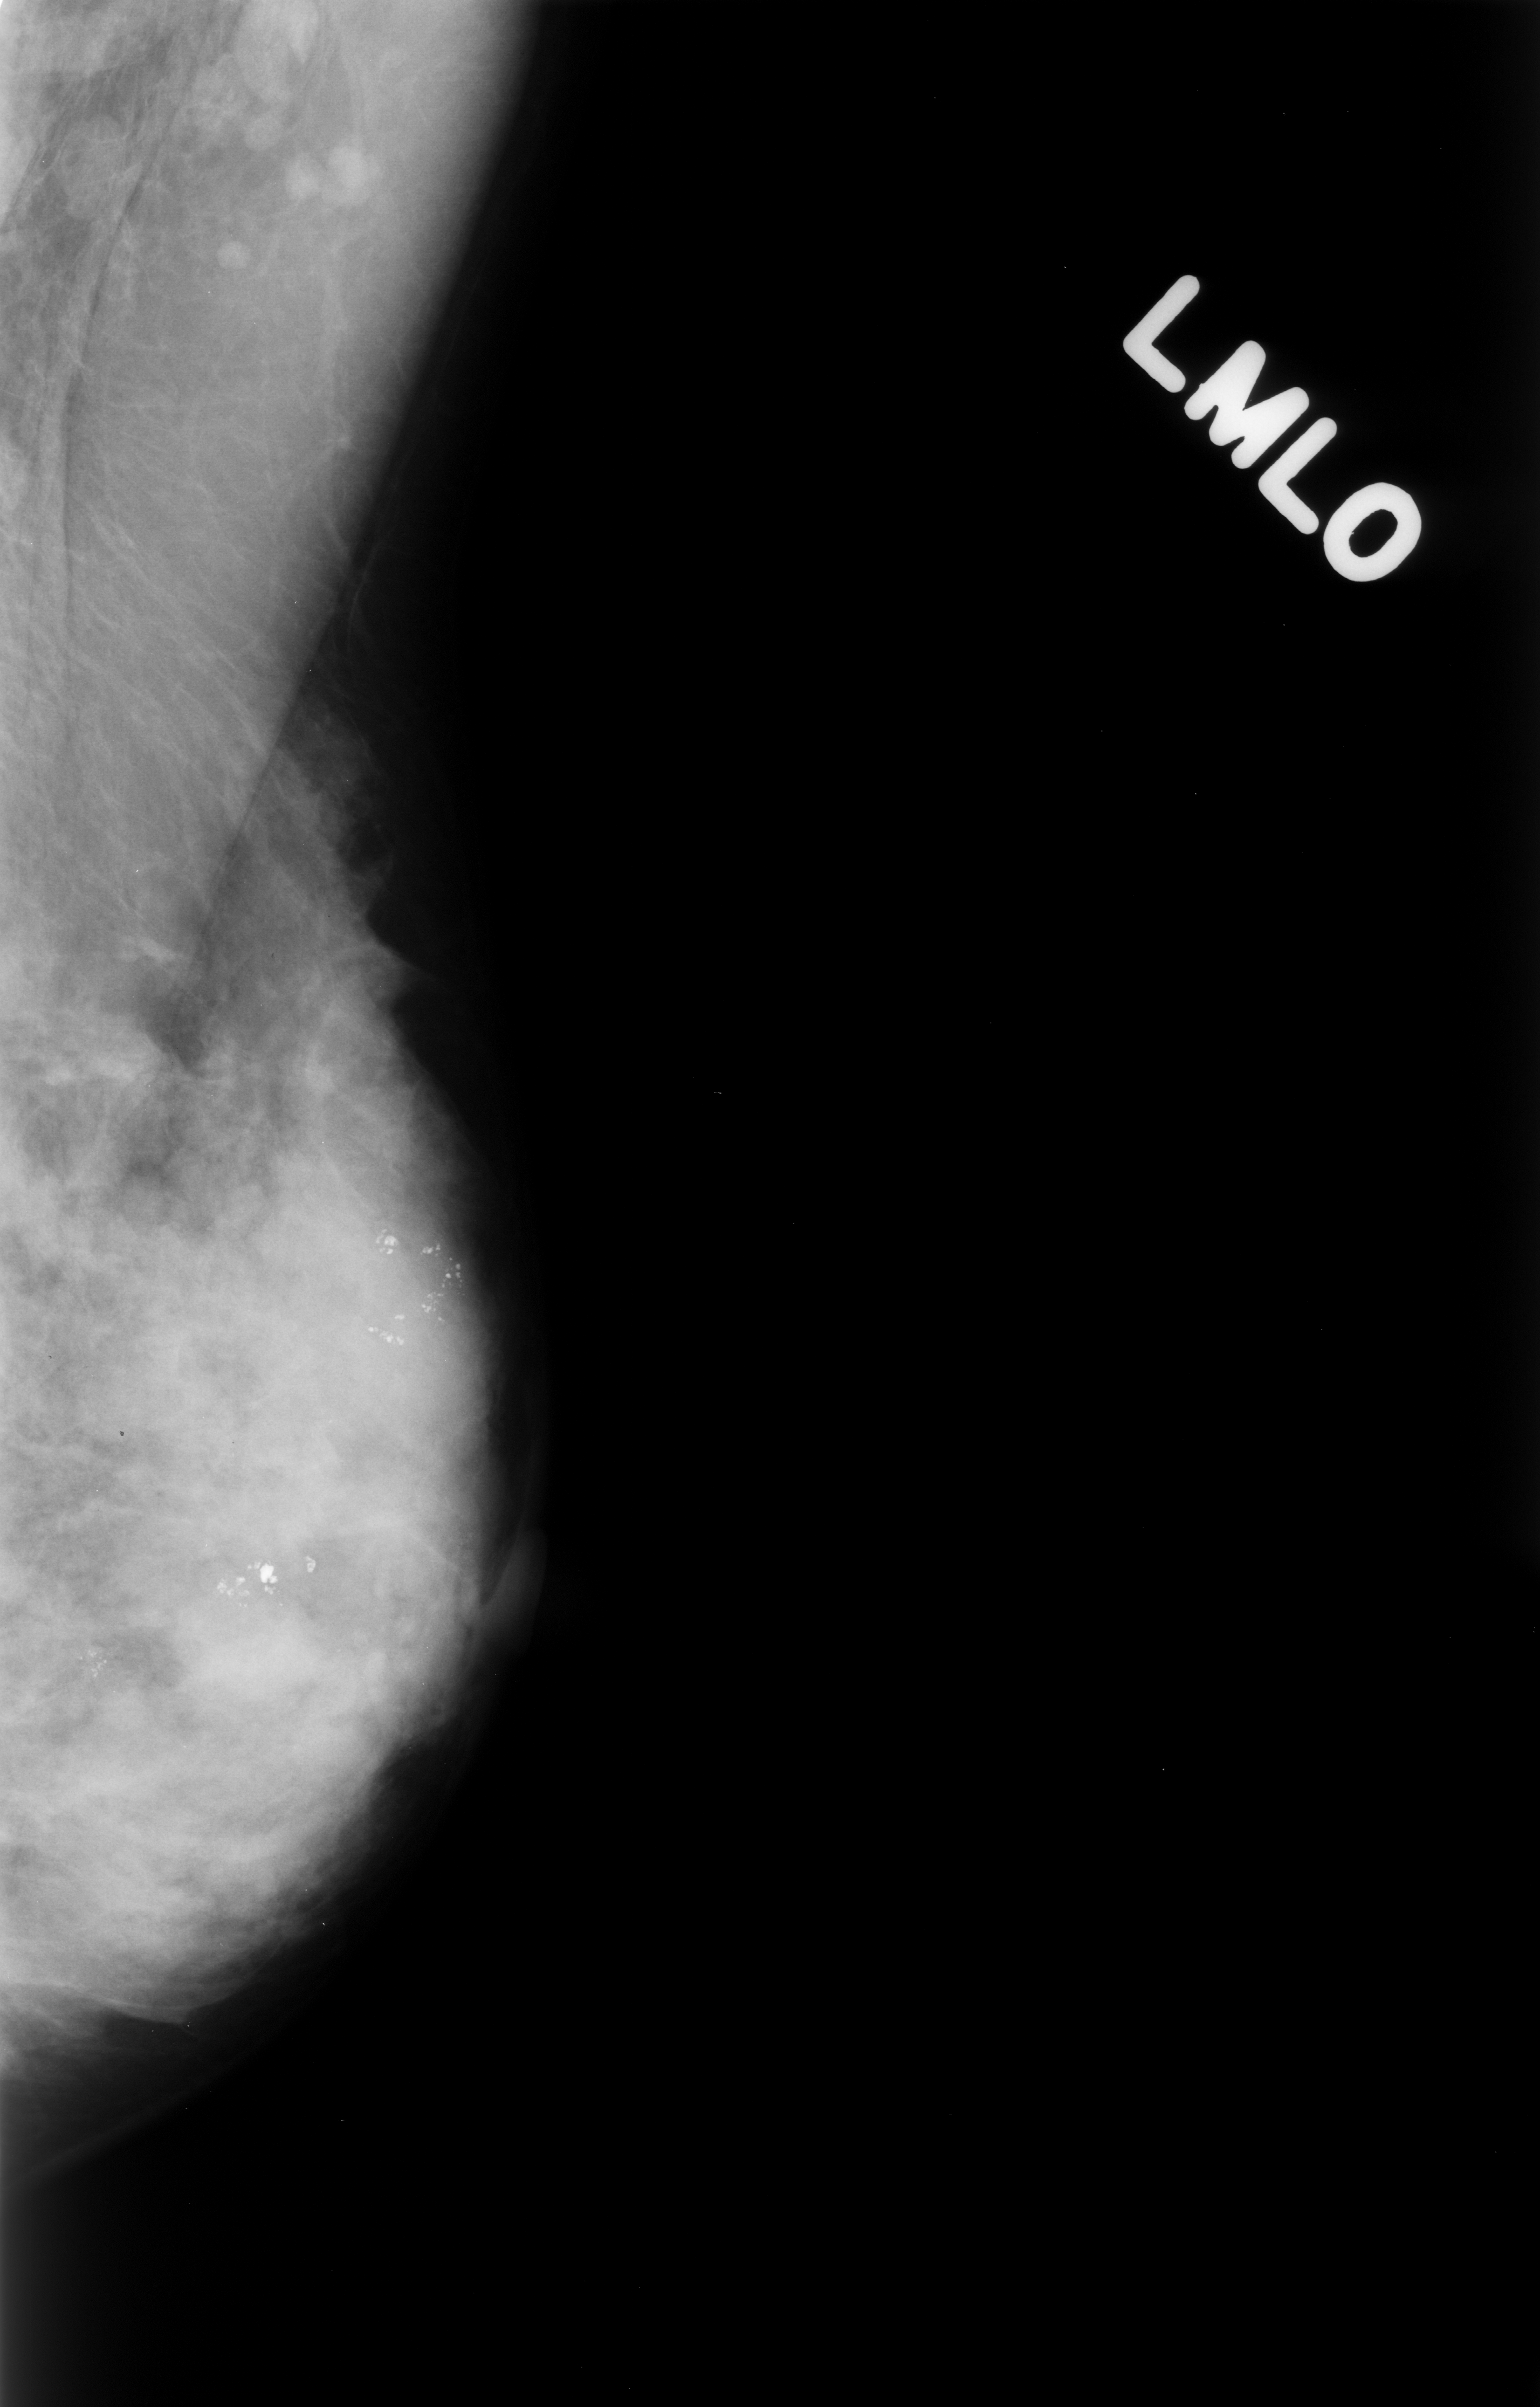
Scanned film-screen mammogram; left breast; mediolateral oblique (MLO) view; breast composition: extremely dense (BI-RADS density category 4 of 4).
Marked findings (only marked abnormalities are described; nothing is implied about the rest of the image): Finding 1 of 3: calcifications, morphology pleomorphic, distribution clustered; BI-RADS assessment category 4; pathology result (as recorded, not read from the image): benign. Finding 2 of 3: calcifications, morphology pleomorphic, distribution clustered; BI-RADS assessment category 4; subtlety rating 5 on a 1 (subtle) to 5 (obvious) scale; pathology (as recorded): benign. Finding 3 of 3: calcifications, morphology pleomorphic, distribution clustered; BI-RADS assessment category 4; subtlety rating 5 on a 1 (subtle) to 5 (obvious) scale; pathology (as recorded): benign.